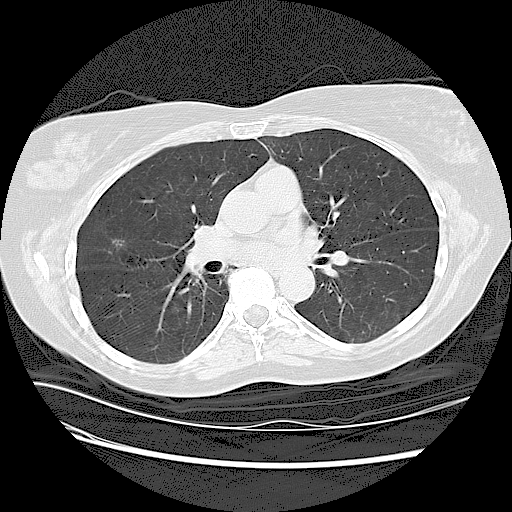
Low-dose screening chest CT, one axial slice; slice 65 of 125 in the series (ordered by position); 120 kVp; lung window (W 1500 / L -600 HU); 512 × 512 image matrix.
Annotated regions visible in this slice (expert manual segmentation):
- lesion 1 (tumor, upper lobe of right lung): bounding box [x1, y1, x2, y2] px = [112, 240, 124, 246]